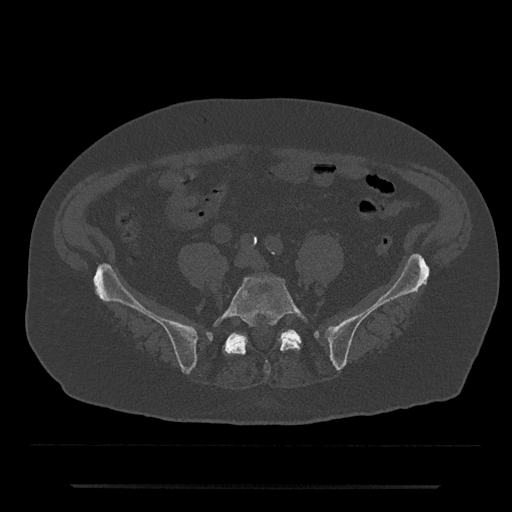
CT including the spine, one axial slice; slice 277 of 797 in the series (ordered by position); reconstruction kernel Br40s/3; bone window (W 1800 / L 400 HU); 0.5 mm slice thickness; 512 × 512 image matrix, field of view 434 × 434 mm. Patient: male, 80 years. From the clinical record (not read from this slice): primary cancer: prostate.
Annotated regions visible in this slice (semi-automatically segmented with operator editing):
- L5 vertebra: bounding box (x1, y1, x2, y2) in pixels: (213, 276, 305, 374)